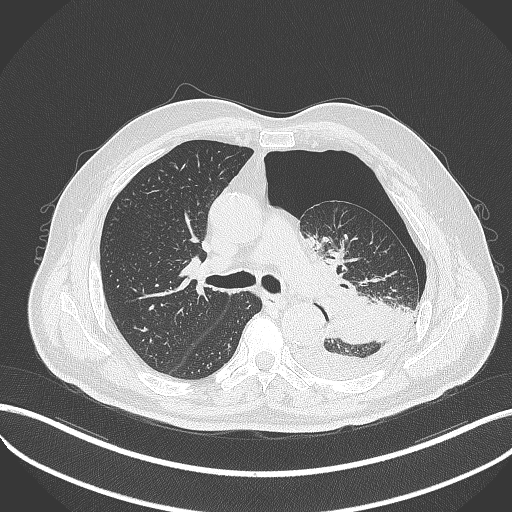
Chest CT, one axial slice; position 326 of 464 along the scan axis; 120 kVp; lung window (W 1500 / L -600 HU); 1 mm slice thickness; 512 × 512 image matrix, field of view 400 × 400 mm. Male patient, age 76 years. Case-level facts recorded for this patient, not image findings: clinical TNM (as recorded): T3 N0 M1b.
Structures marked on this image (rectangle marked by the reading radiologist):
- lung tumour (recorded histology: adenocarcinoma): box from (x=327, y=290) to (x=395, y=346) px